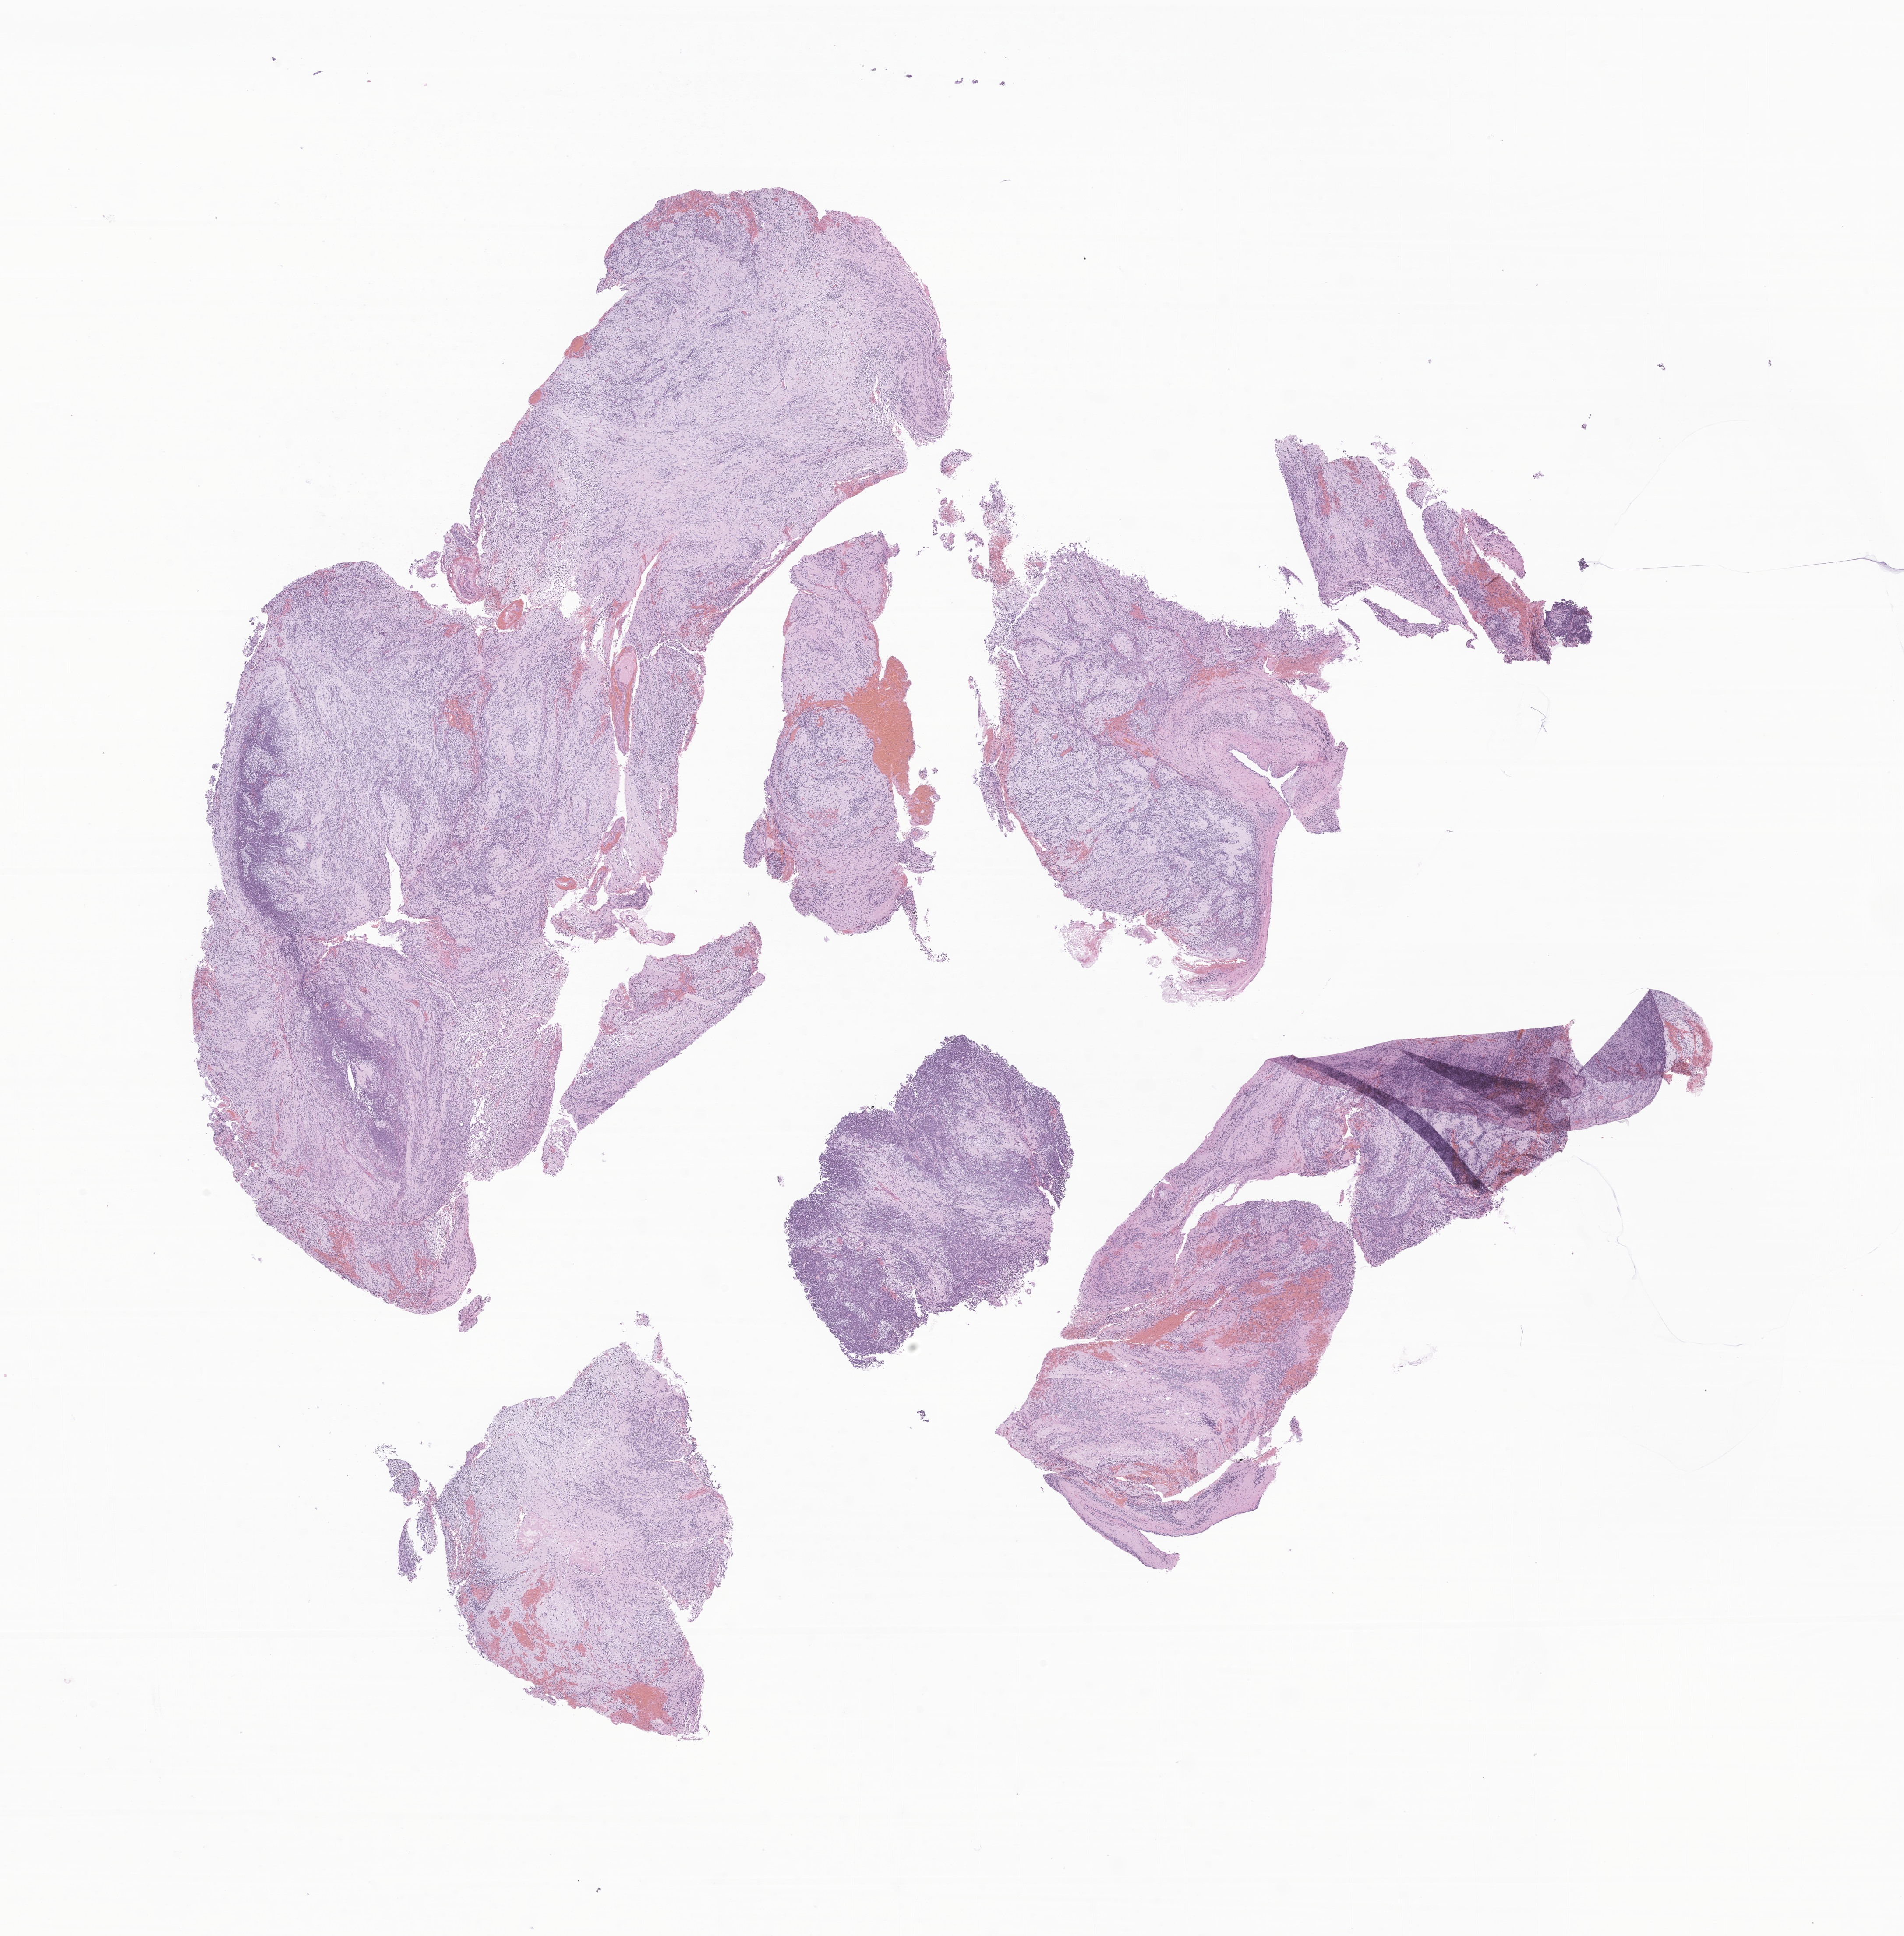
Haematoxylin and eosin whole-slide image of tumor tissue from the brain — shown as a low-resolution overview of the whole scanned area (about 18.3 x 18.6 mm), formalin-fixed paraffin-embedded section. Patient: female, age 58 months (4 years 10 months).
* recorded diagnosis: Medulloblastoma, NOS